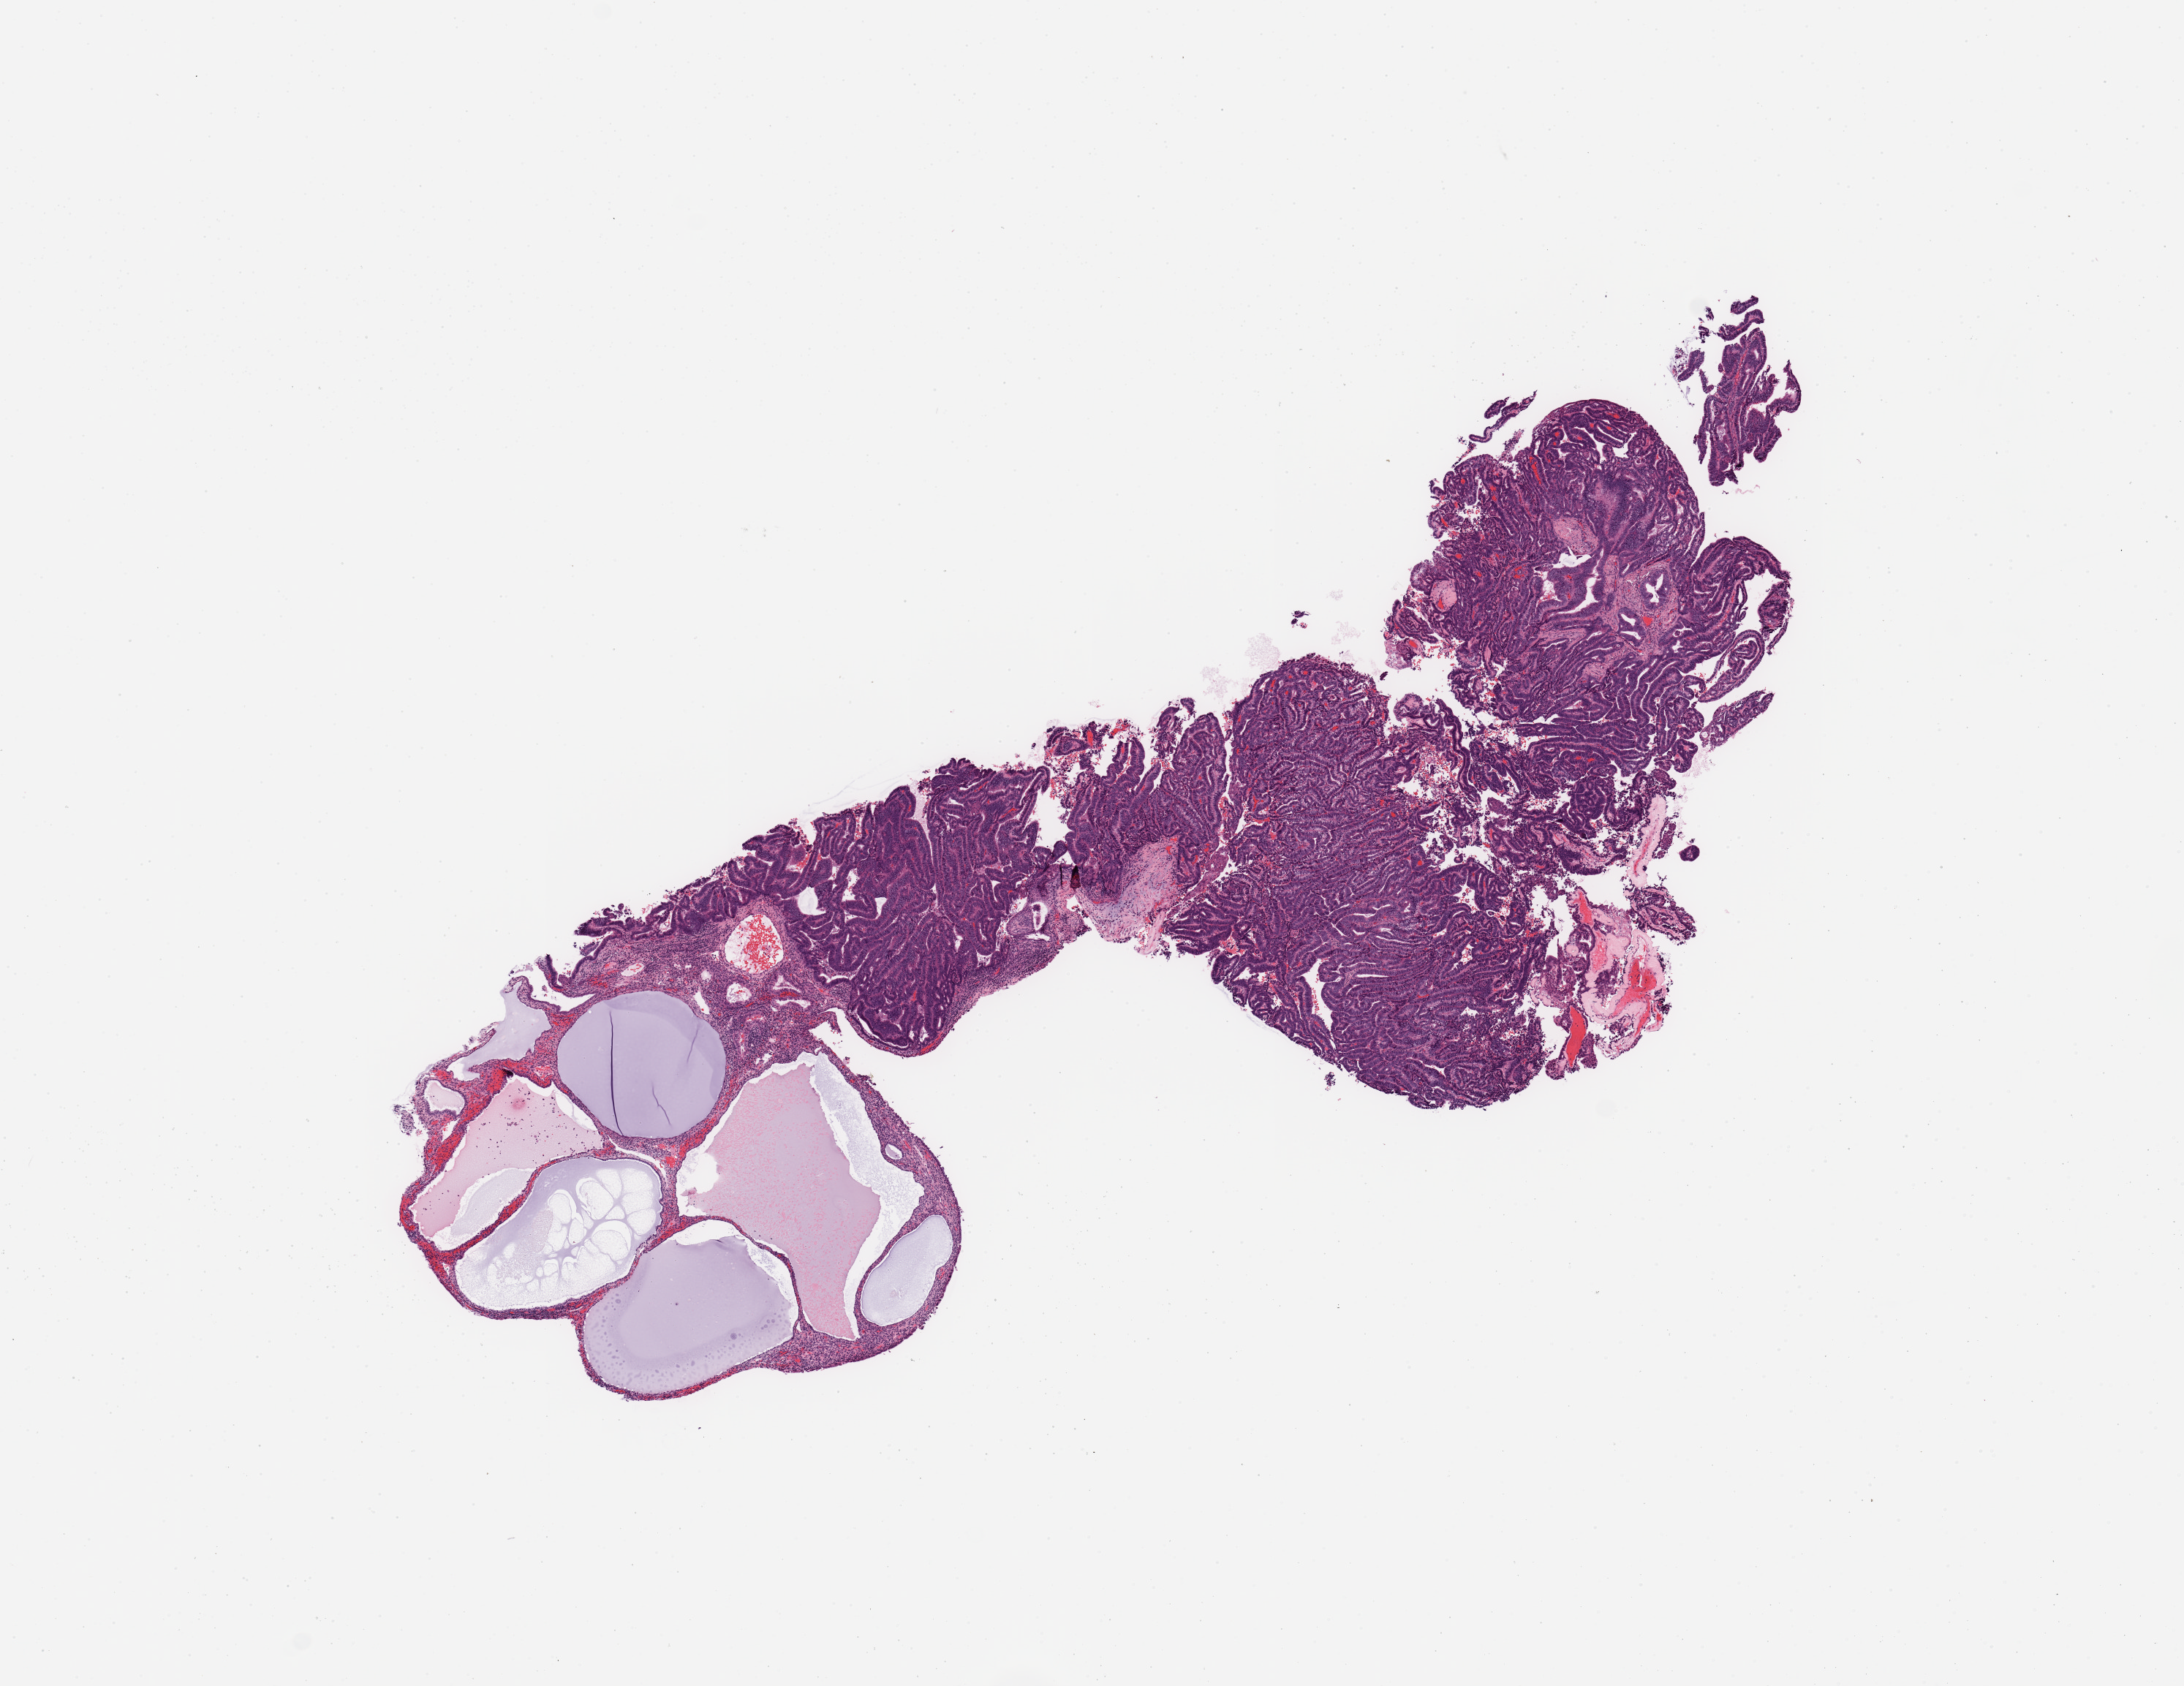
H&E whole-slide image, low-resolution overview of the scanned area, about 11.8 x 9.1 mm, uterus, tumour tissue. 62-year-old female patient.
Diagnosis: Endometrioid adenocarcinoma, NOS.